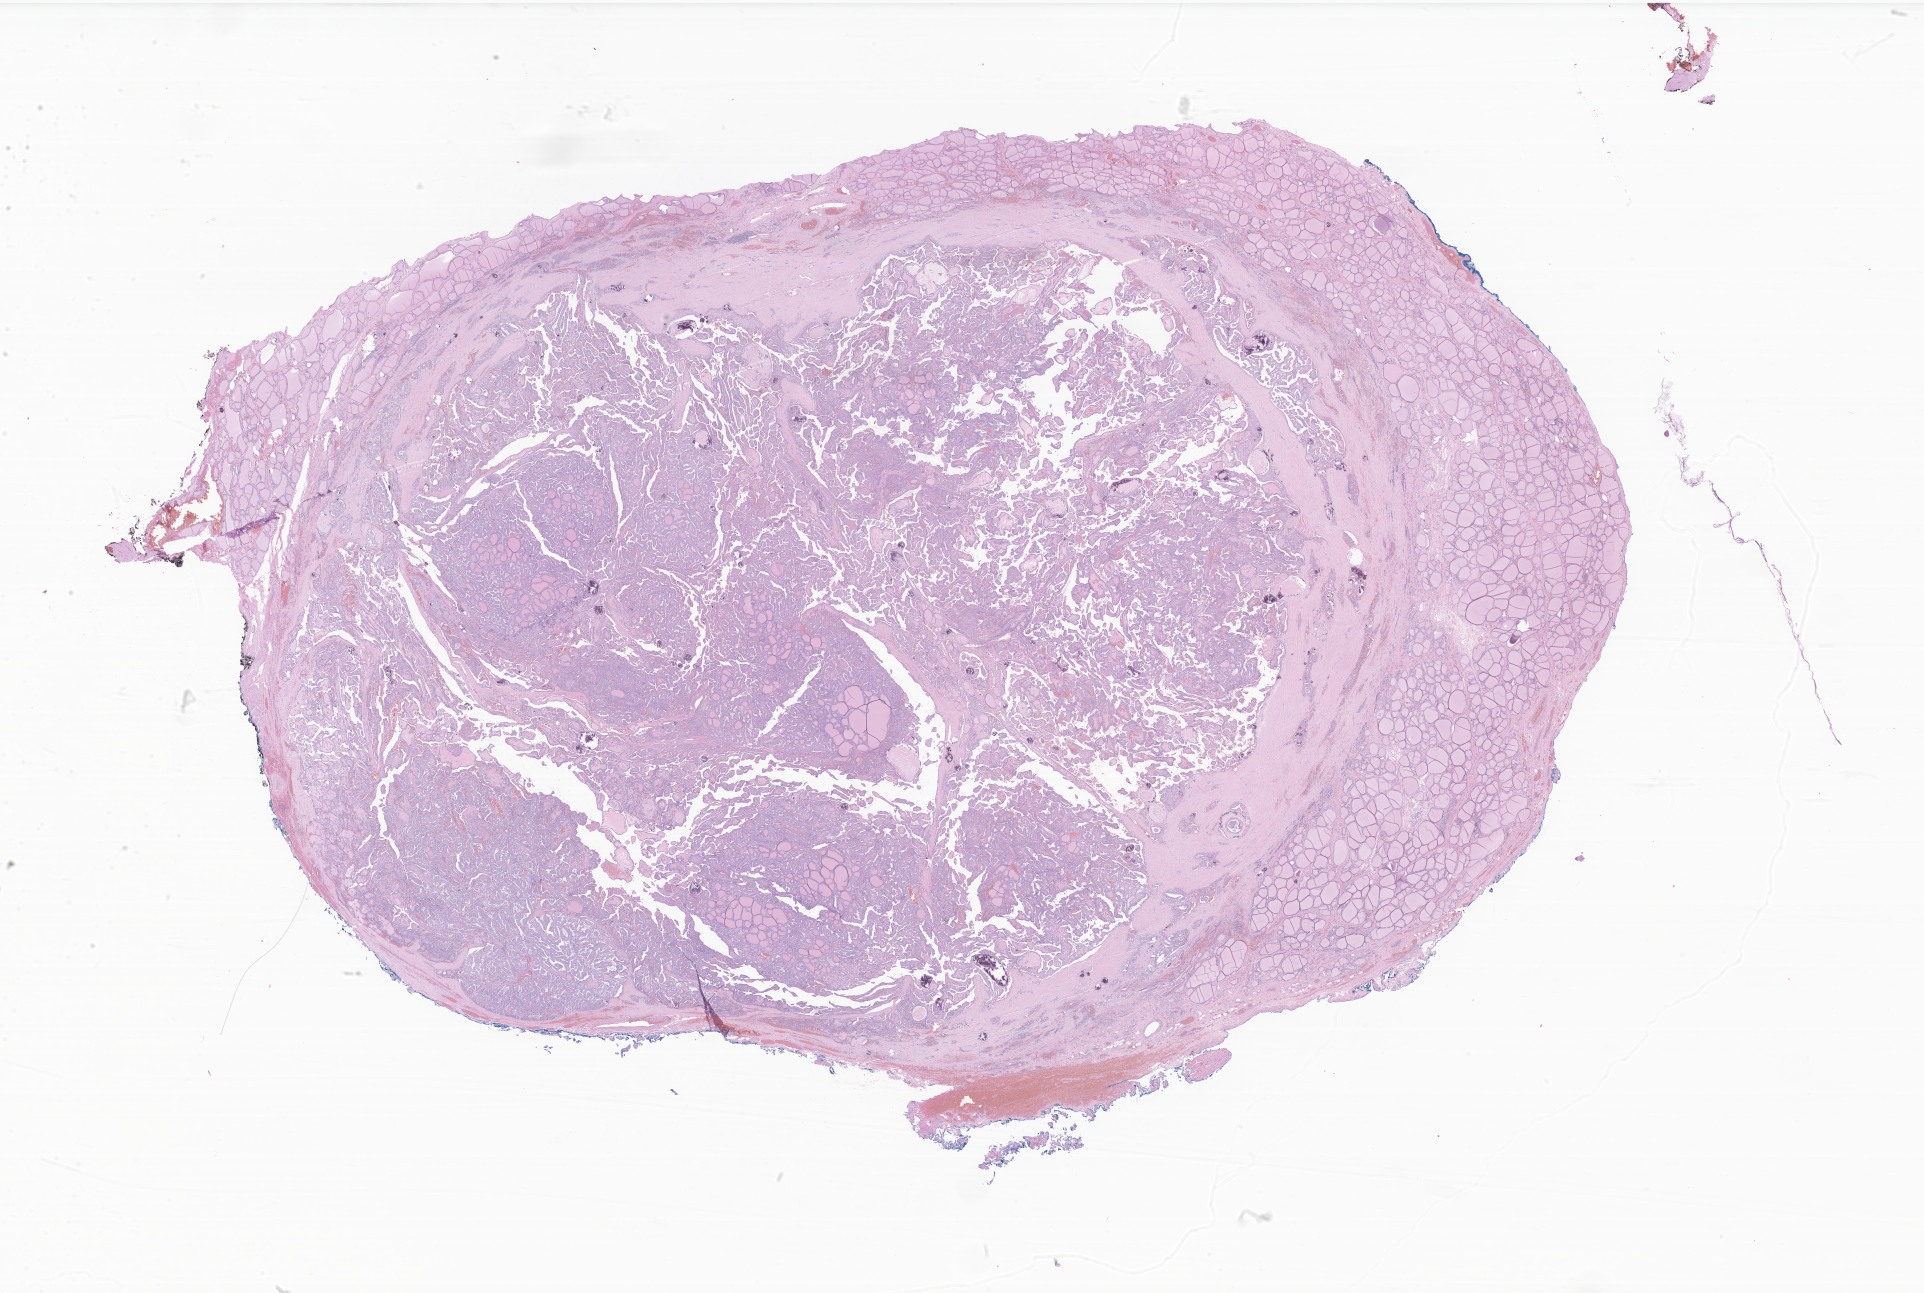
Whole-slide image, hematoxylin and eosin (H&E) stain of tumor tissue from the thyroid — low-resolution overview of the scanned area, about 32.4 x 21.8 mm; formalin-fixed paraffin-embedded section. Patient: female, age 146 months (12 years 2 months).
Diagnosis (ICD-O-3 morphology term): Papillary carcinoma, NOS.